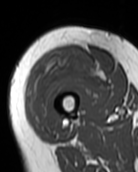
MRI of an extremity soft-tissue mass, one axial slice; slice 29 of 99 in the series (ordered by position); MR volume resampled by the dataset authors to the PET/CT grid (not the native acquisition matrix); 3.27 mm slice thickness; 138 × 172 image matrix, field of view 135 × 168 mm. Female patient. Case-level facts recorded for this patient, not image findings: histological type: pleiomorphic undifferentiated sarcoma; grade: high; site of the primary tumour: right quadricep.
Outlined on this slice (expert contour drawn on MRI and transferred to this co-registered scan by the dataset authors):
- gross tumour volume including surrounding oedema: bounding box [x1, y1, x2, y2] px = [28, 52, 106, 126]